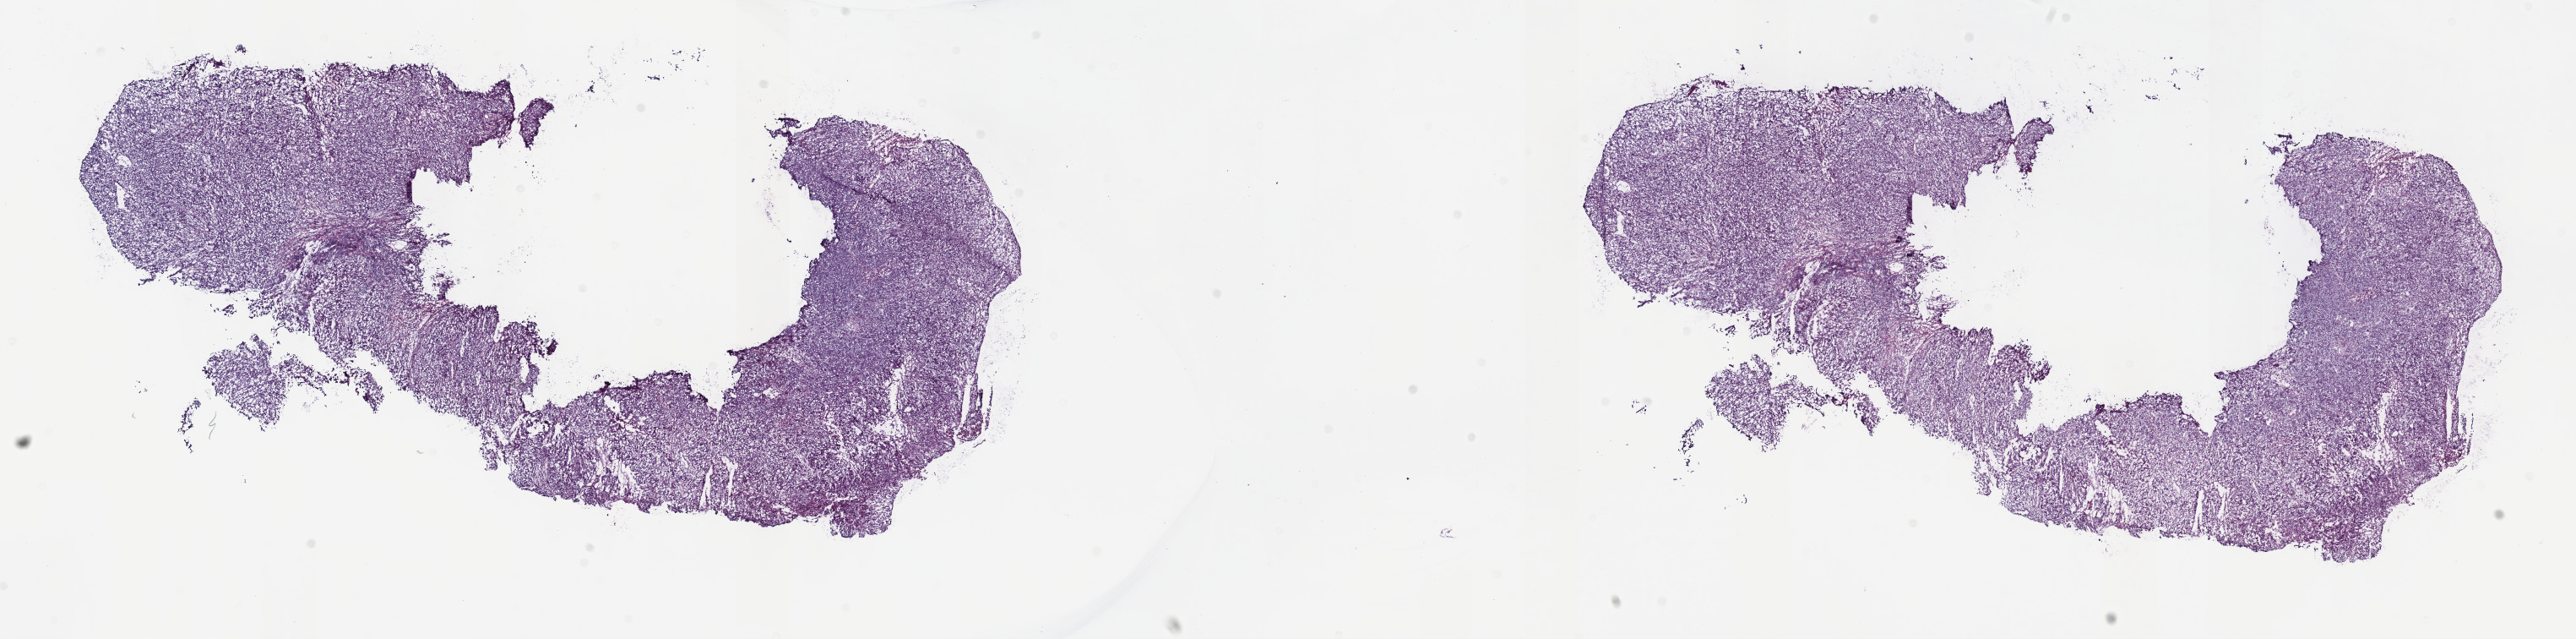
Whole-slide histology image, Hematoxylin and eosin (H&E) stained, shown as a low-resolution overview of the whole scanned area (about 24.7 x 6.1 mm, slide scanned at 40x). Frozen section from the top of the tissue portion. Cervix, primary tumour sample. Patient: female, age at initial diagnosis 47 years. Histologic grade: G2 (moderately differentiated). Composition of this section per pathologist review: tumour cells 70%, tumour nuclei 70%, normal cells 10%, stromal cells 15%, necrosis 5%. Inflammatory infiltration, as recorded: lymphocyte infiltration 8%, monocyte infiltration 1%, neutrophil infiltration 1%.
FIGO stage: IB2. Pathologic diagnosis: Squamous cell carcinoma, NOS.